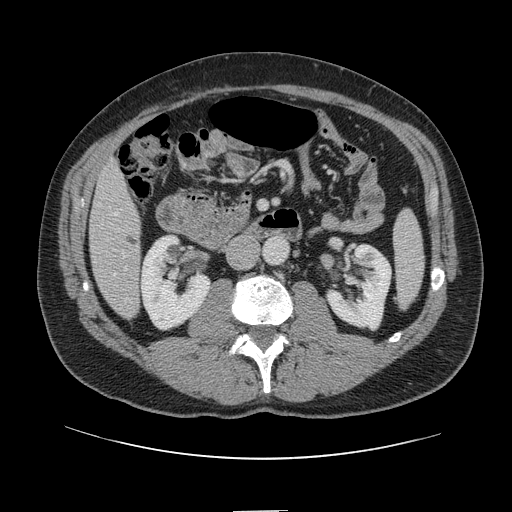
Contrast-enhanced abdominal CT, one axial slice. Slice 30 of 161 in the series (ordered by position). 120 kVp. Intravenous contrast given. Soft-tissue window (W 400 / L 40 HU). 2.5 mm slice thickness. 512 × 512 image matrix, field of view 412 × 412 mm. Male patient, age 66 years. Case-level facts recorded for this patient, not image findings: diagnosis: colorectal cancer liver metastases, imaged before liver resection; multiple liver metastases: no; largest metastasis: 3.5 cm; disease in both lobes: no.
Annotated regions visible in this slice (manually delineated by an expert):
- hepatic veins: box from (x=115, y=213) to (x=118, y=275) px
- liver: (x=91, y=164)–(x=141, y=319)
- planned liver remnant (the part of the liver to remain after resection): (x=91, y=164)–(x=141, y=260)